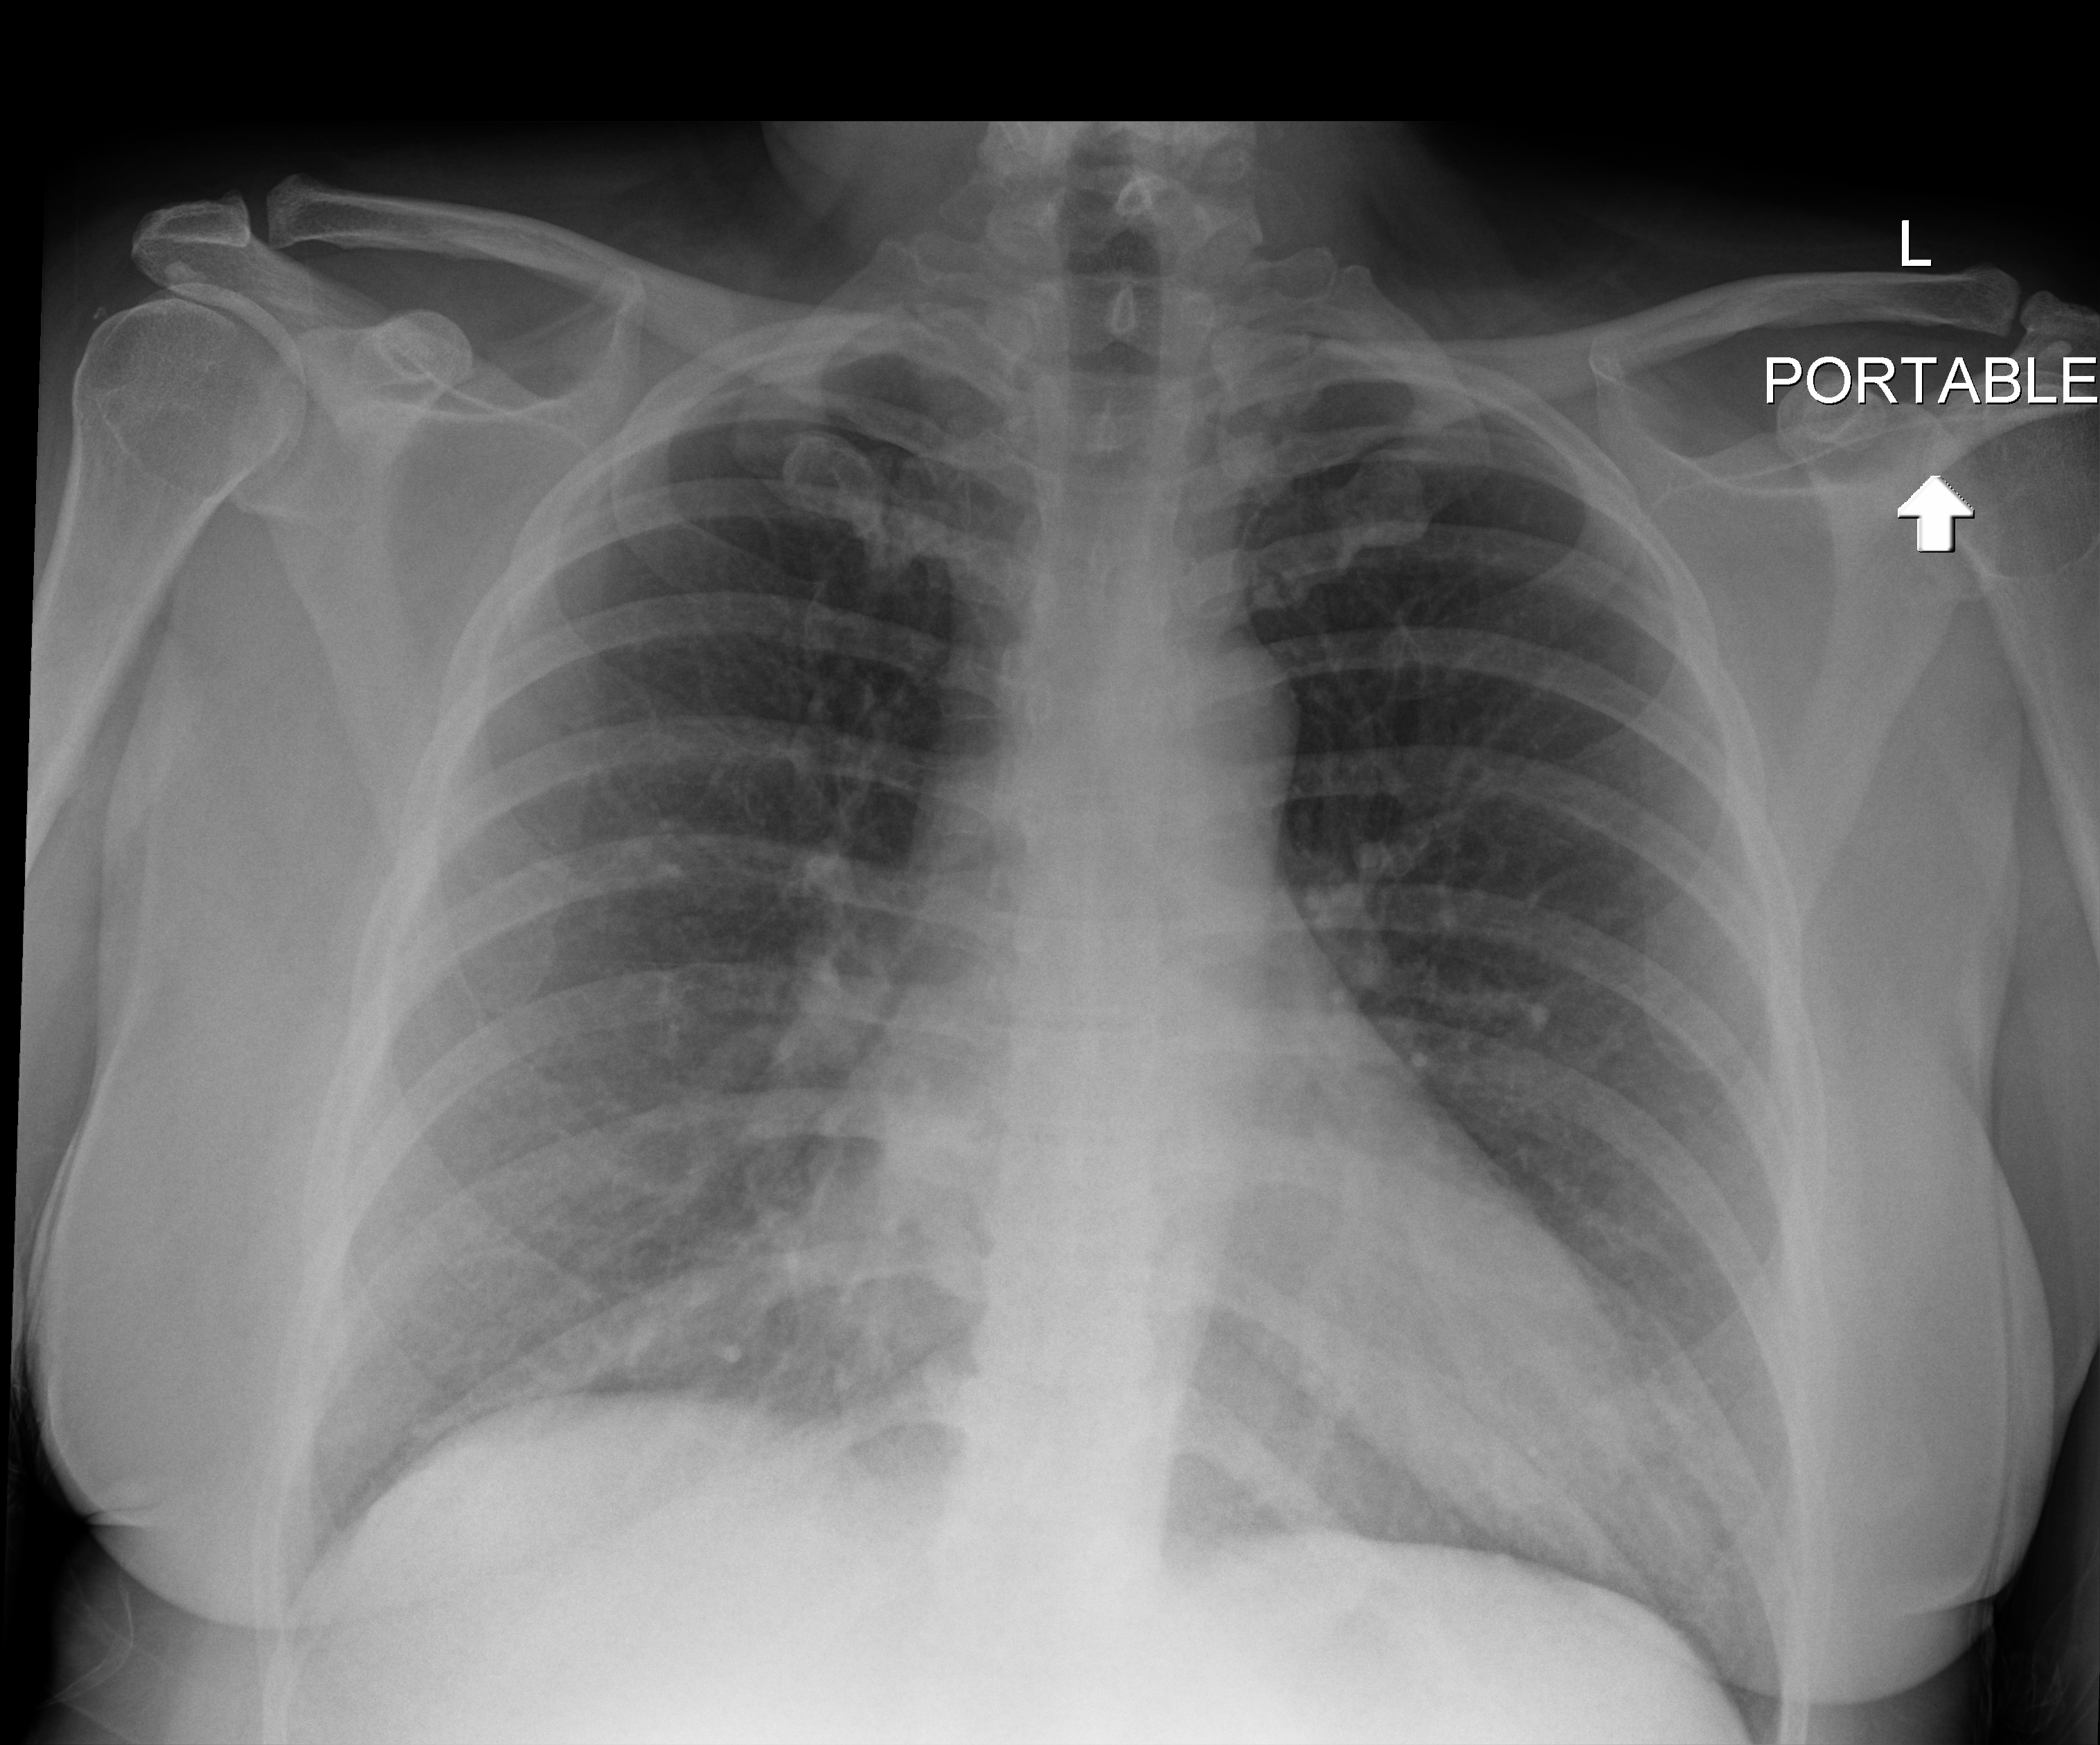
Chest X-ray, anteroposterior (AP) projection. Patient hospitalised with COVID-19; female, aged 18–59 years.
Admission-level facts for this patient (not findings on this image; timing relative to this image not recorded): admitted to intensive care during this hospital stay: no; mechanically ventilated during this hospital stay: no.